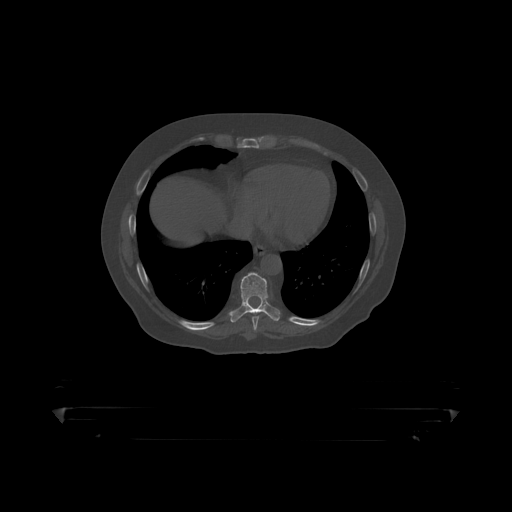
CT including the spine, one axial slice. Slice 241 of 390 in the series (ordered by position). Reconstruction kernel STANDARD. 120 kVp. Bone window (W 1800 / L 400 HU). 1.25 mm slice thickness. 512 × 512 image matrix, field of view 650 × 650 mm. Patient: male, 60 years. Case-level facts recorded for this patient, not image findings: primary cancer: prostate.
Outlined on this slice (semi-automatic segmentation, software-assisted and operator-edited):
- T8 vertebra: bounding box [x1, y1, x2, y2] px = [252, 317, 259, 319]
- T9 vertebra: [231, 273, 281, 318]